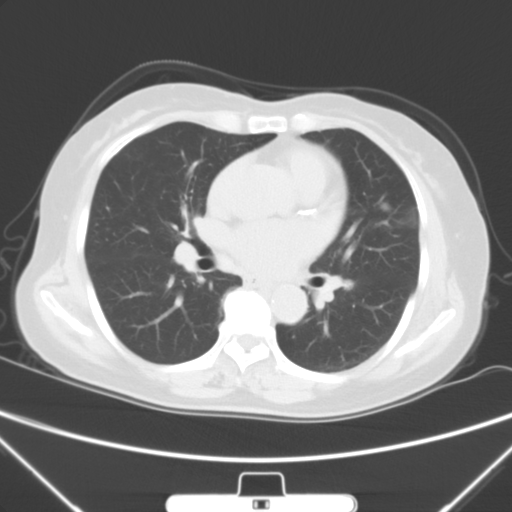
Chest CT, one axial slice. Slice 29 of 60 in the series (ordered by position). 120 kVp. Lung window (W 1500 / L -600 HU). 512 × 512 image matrix, field of view 350 × 350 mm. Female patient, age 70 years. Case-level facts recorded for this patient, not image findings: clinical TNM (as recorded): T1b N0 M0; histopathological grade: G2.
Structures marked on this image (bounding box drawn by a radiologist):
- lung tumour (recorded histology: adenocarcinoma): box from (x=375, y=192) to (x=395, y=224) px